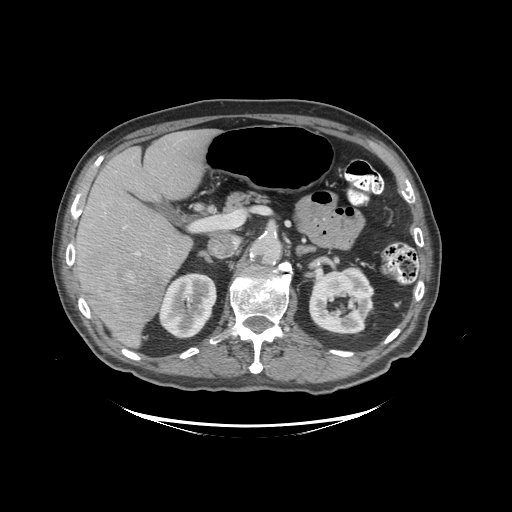
Contrast-enhanced abdominal CT (liver protocol), one axial slice. Slice 55 of 99 in the series (ordered by position). Reconstruction kernel STANDARD. 140 kVp. Soft-tissue window (W 400 / L 40 HU). 2.5 mm slice thickness. 512 × 512 image matrix. From the clinical record (not read from this slice): diagnosis: hepatocellular carcinoma (patient treated with transarterial chemoembolisation; whether this scan precedes or follows treatment is not stated here); TNM stage (as recorded): Stage-I; Child-Pugh class: A; tumour differentiation: moderately differentiated; tumour nodularity: uninodular.
Annotated regions visible in this slice (semi-automatically segmented with operator editing):
- liver parenchyma outside the tumour (the mass and vessels are separate outlines, so this box may not span the whole liver): bounding box (x1, y1, x2, y2) in pixels: (72, 128, 216, 346)
- mass: (86, 255, 163, 333)
- liver vessels: (73, 250, 140, 255)